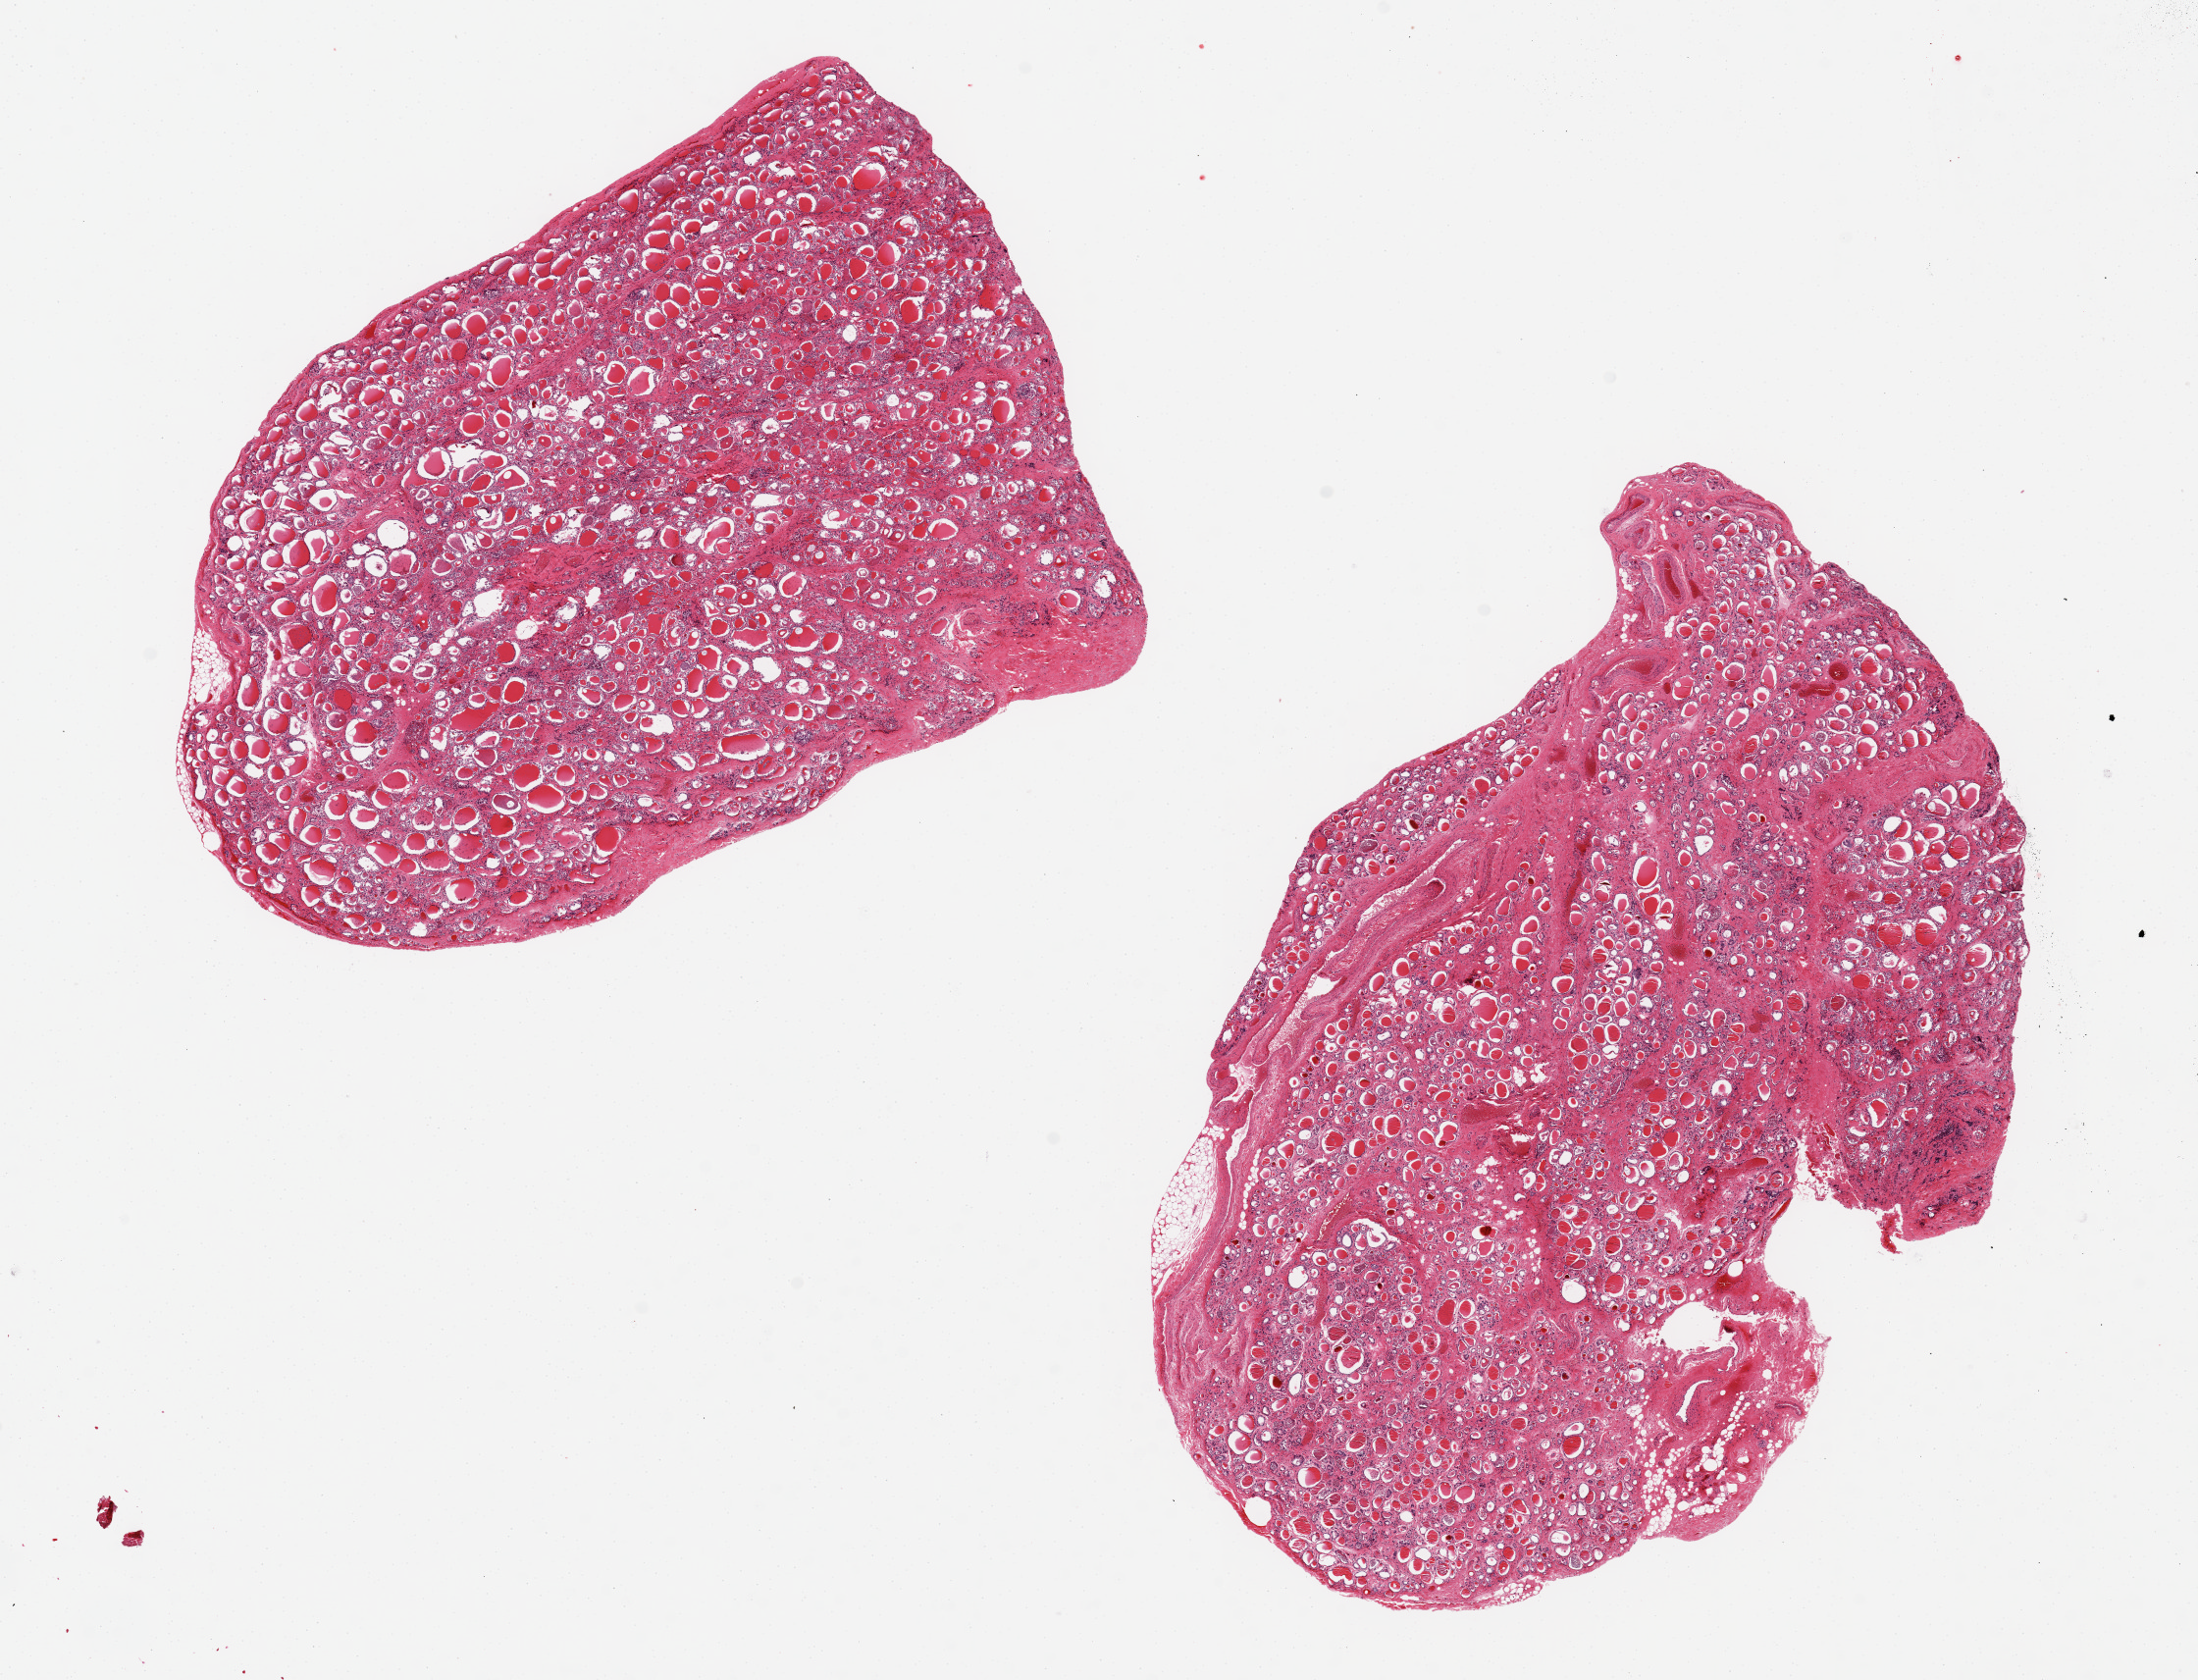
Digitized hematoxylin and eosin (H&E)-stained section, brightfield, whole scanned area (about 17.7 x 13.5 mm) shown as a low-resolution overview. PAXgene-fixed paraffin-embedded (PFPE) section. Target tissue: thyroid. Donor tissue sample.
• review note (as recorded): 2 pieces,9x6 & 8x5 mm